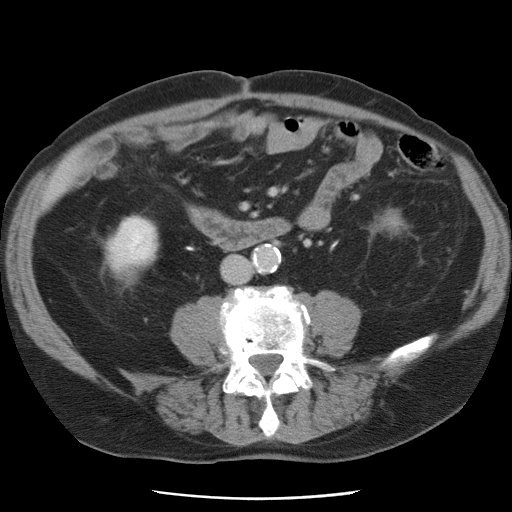
Contrast-enhanced abdominal CT, one axial slice; slice 10 of 78 in the series (ordered by position); intravenous contrast given; soft-tissue window (W 400 / L 40 HU); 512 × 512 image matrix, field of view 337 × 337 mm. Male patient, age 75 years. From the clinical record (not read from this slice): diagnosis: colorectal cancer liver metastases, imaged before liver resection; multiple liver metastases: yes; largest metastasis: 2.4 cm; disease in both lobes: yes.
Outlined on this slice (expert manual segmentation):
- liver: bounding box [x1, y1, x2, y2] px = [46, 165, 70, 202]
- planned liver remnant (the part of the liver to remain after resection): [46, 164, 72, 202]